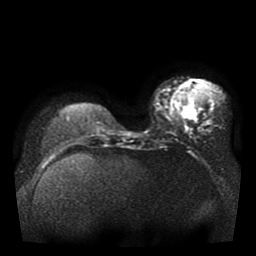
Breast MRI, one axial slice. Slice 14 of 41 in the series (ordered by position). Diffusion-weighted series; image 2 of 4 stored at this slice position (different b-values; order by instance number). 1.5 T. 5 mm slice thickness. 256 × 256 image matrix, field of view 330 × 330 mm. Female patient.
Outlined on this slice (expert manual segmentation):
- tumour on diffusion-weighted imaging: bounding box <186,110,196,120> (left, top, right, bottom; pixels)